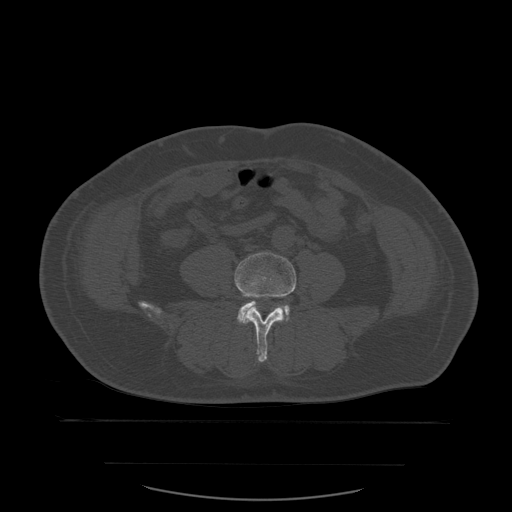
CT including the spine, one axial slice. Position 158 of 590 along the scan axis. Bone window (W 1800 / L 400 HU). 1.25 mm slice thickness. 512 × 512 image matrix, field of view 479 × 479 mm. Patient age 71 years. Case-level facts recorded for this patient, not image findings: primary cancer: lung; vertebrae with lytic lesions (as recorded): T1, T2, L5, S1.
Annotated regions visible in this slice (semi-automatic segmentation, software-assisted and operator-edited):
- L4 vertebra: bounding box [x1, y1, x2, y2] px = [235, 253, 297, 362]
- L5 vertebra: [237, 297, 290, 324]